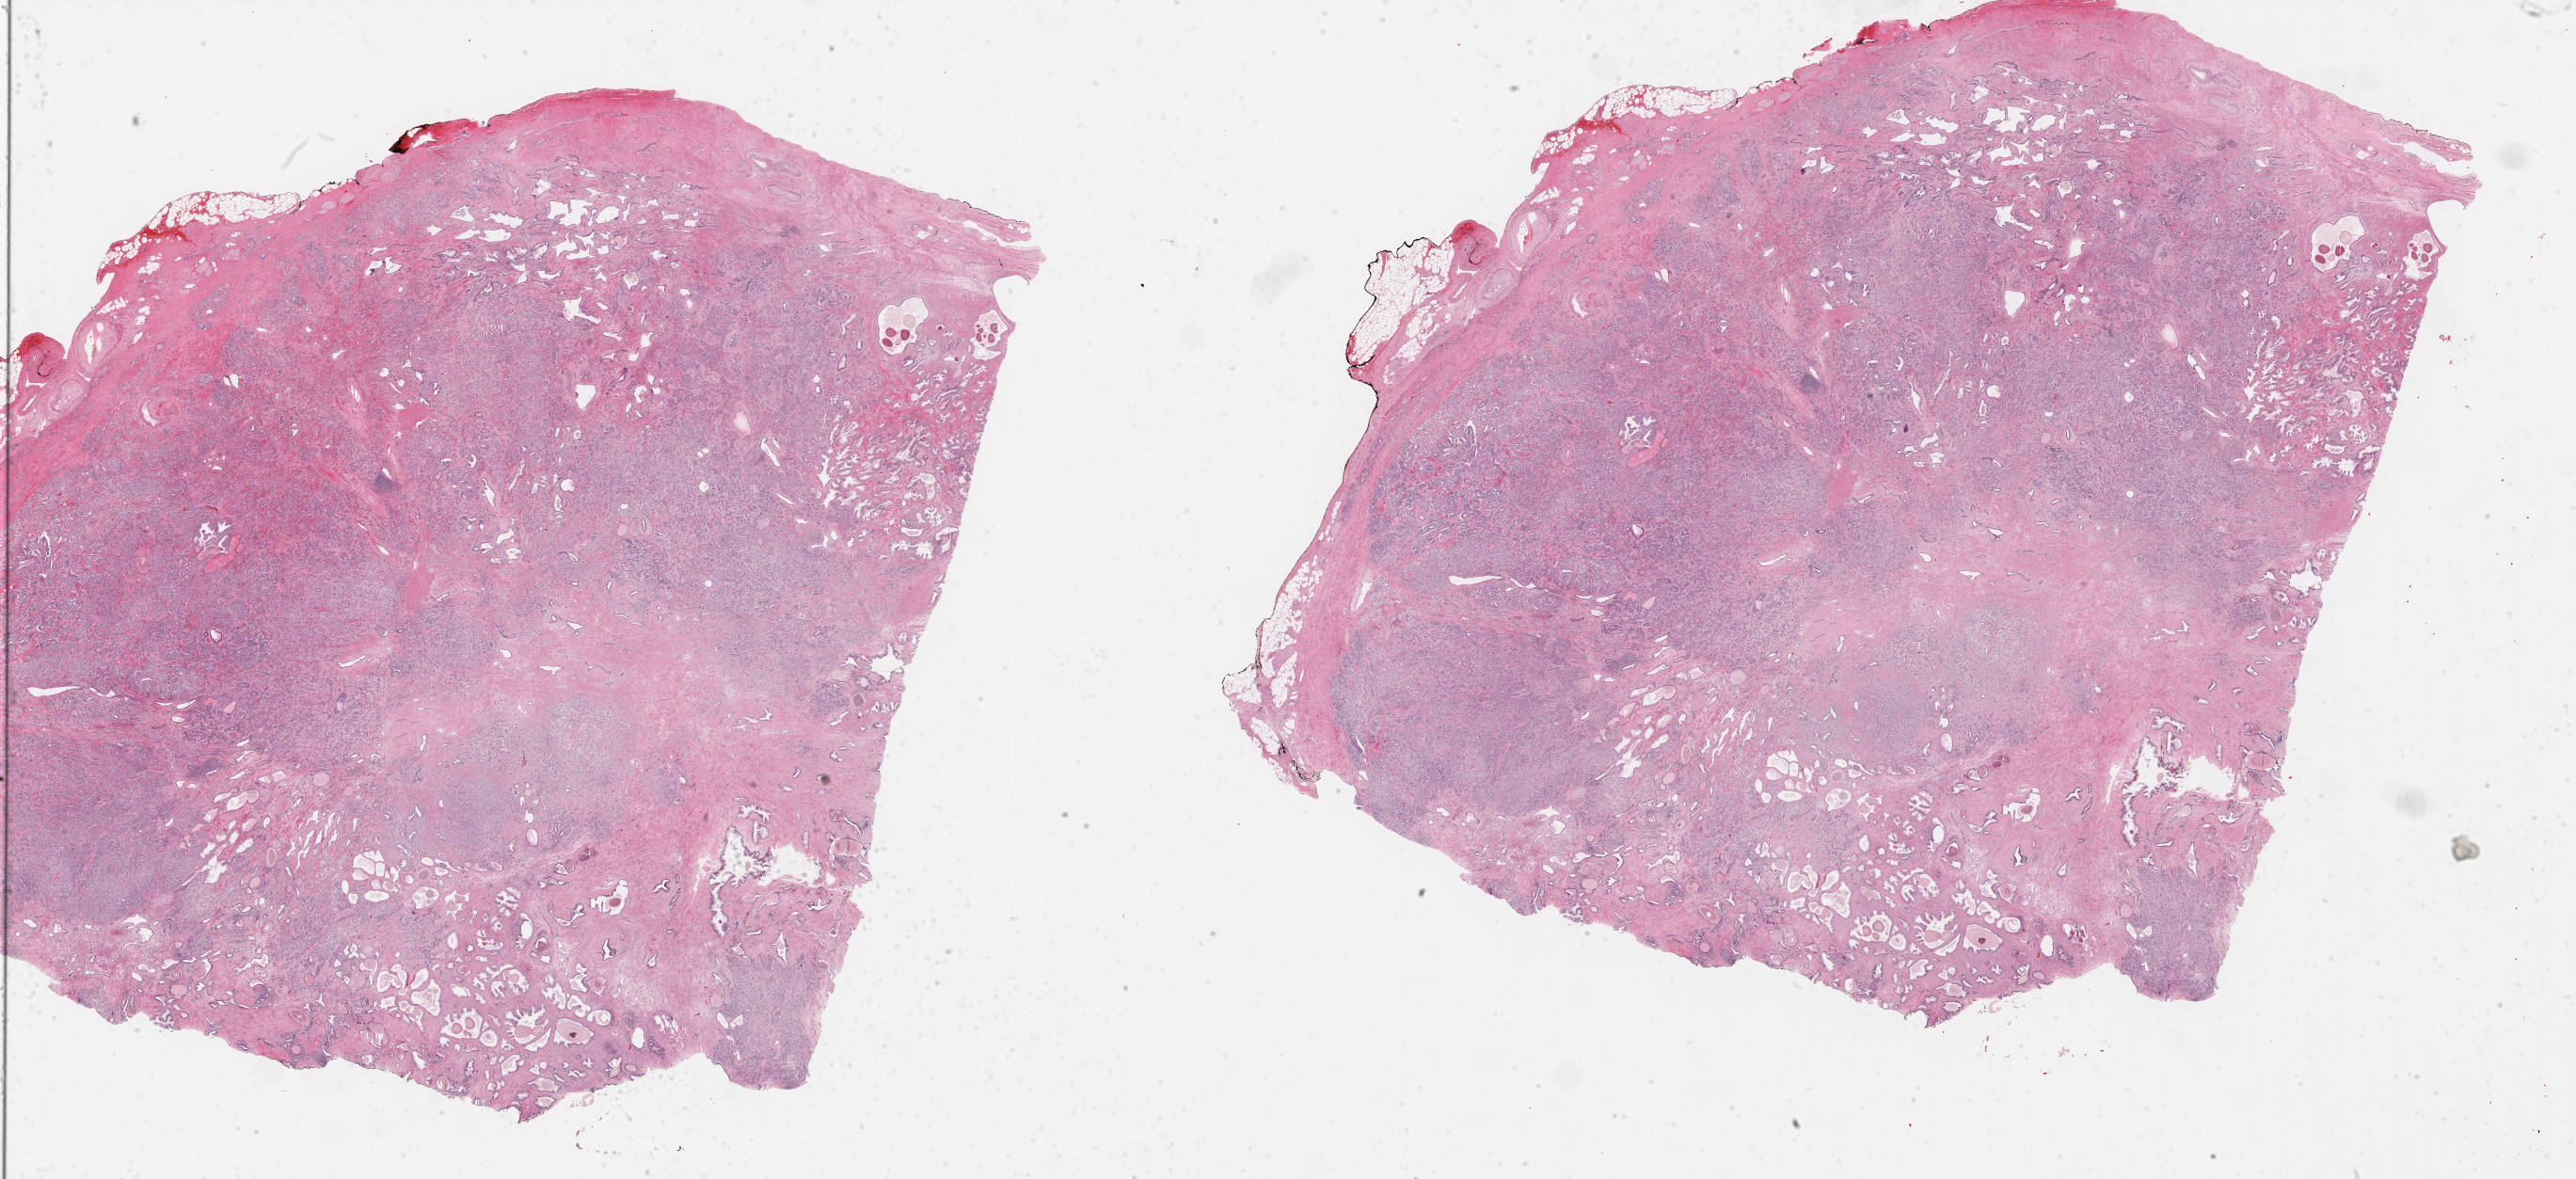
H&E-stained whole-slide image — shown as a low-resolution overview of the whole scanned area (about 44.3 x 20.3 mm). FFPE section. Prostate, primary tumour sample. Male, age 65 years at initial diagnosis. Gleason score: 9 (4+5).
• pathologic diagnosis: Adenocarcinoma, NOS (prostate gland)
• lymph nodes positive (case pathology): 0 of 3 examined
• laterality: right